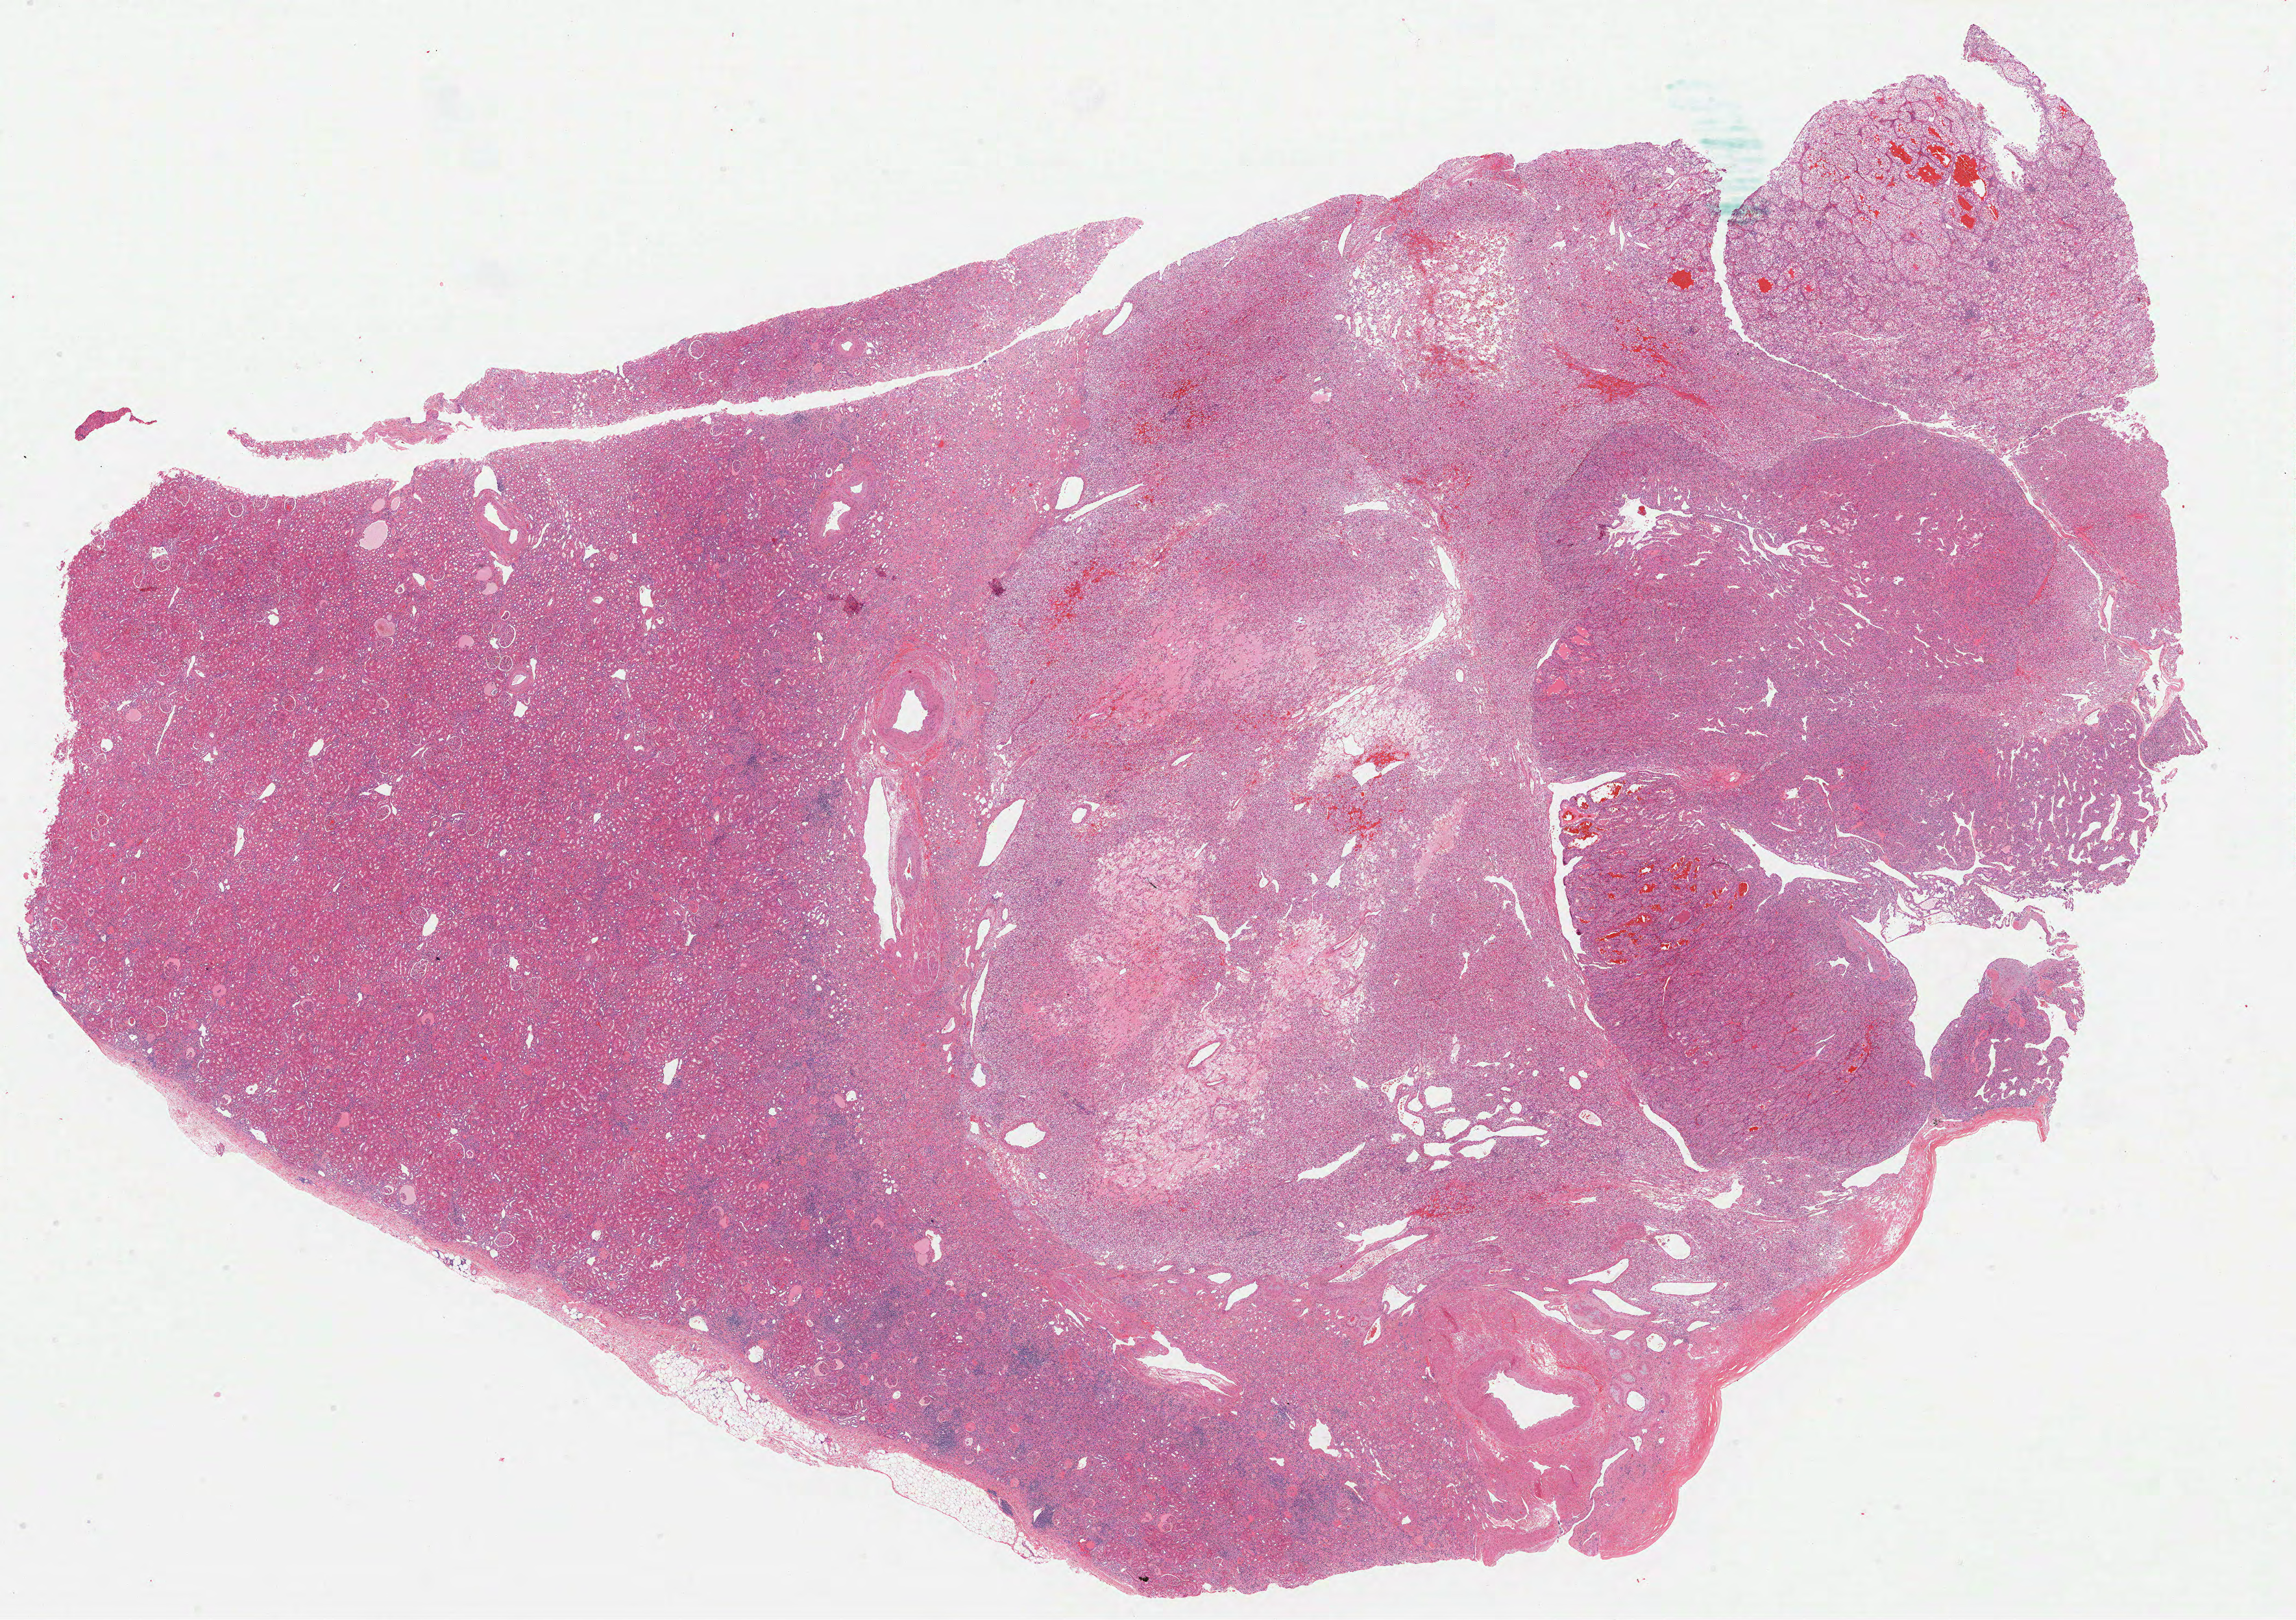
Digitized Hematoxylin and eosin (H&E) stained tissue section (whole slide), low-resolution overview of the scanned area, about 28.5 x 20.1 mm, FFPE section, kidney, primary tumour sample. Patient: female, age at initial diagnosis 72 years. Histologic grade: G3 (poorly differentiated).
- lymph nodes positive (case pathology): 0 of 2 examined
- laterality: left
- AJCC pathologic stage: II
- pathologic diagnosis: Clear cell adenocarcinoma, NOS